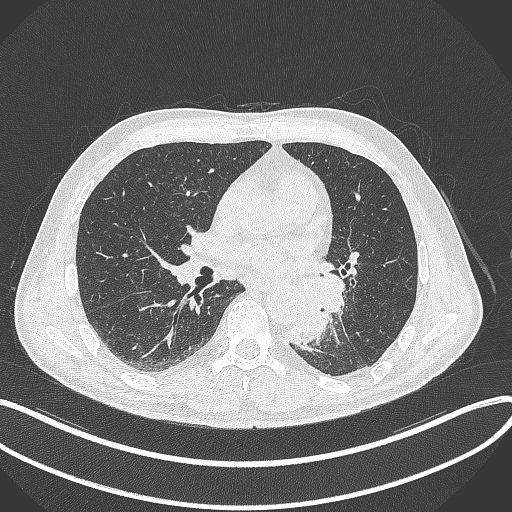
Chest CT, one axial slice. Position 165 of 329 along the scan axis. Reconstruction kernel B70f. 120 kVp. Lung window (W 1500 / L -600 HU). 512 × 512 image matrix, field of view 400 × 400 mm. Male patient, age 59 years. Case-level facts recorded for this patient, not image findings: clinical TNM (as recorded): T2a N2 M0.
Outlined on this slice (rectangle marked by the reading radiologist):
- lung tumour (recorded histology: squamous cell carcinoma): box from (x=283, y=270) to (x=348, y=346) px